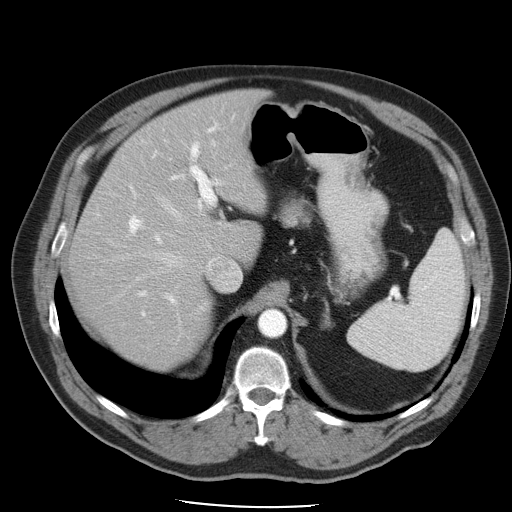
Contrast-enhanced abdominal CT, one axial slice. Slice 34 of 49 in the series (ordered by position). 120 kVp. Soft-tissue window (W 400 / L 40 HU). 5 mm slice thickness. 512 × 512 image matrix, field of view 395 × 395 mm. Male patient, age 68 years. Case-level facts recorded for this patient, not image findings: diagnosis: colorectal cancer liver metastases, imaged before liver resection; multiple liver metastases: yes; largest metastasis: 1.7 cm; chemotherapy before resection: yes.
Annotated regions visible in this slice (expert manual segmentation):
- hepatic veins: bounding box (x1, y1, x2, y2) in pixels: (106, 141, 241, 298)
- liver: (70, 91, 264, 368)
- planned liver remnant (the part of the liver to remain after resection): (70, 91, 263, 368)
- portal vein (with intrahepatic branches): (129, 118, 234, 316)